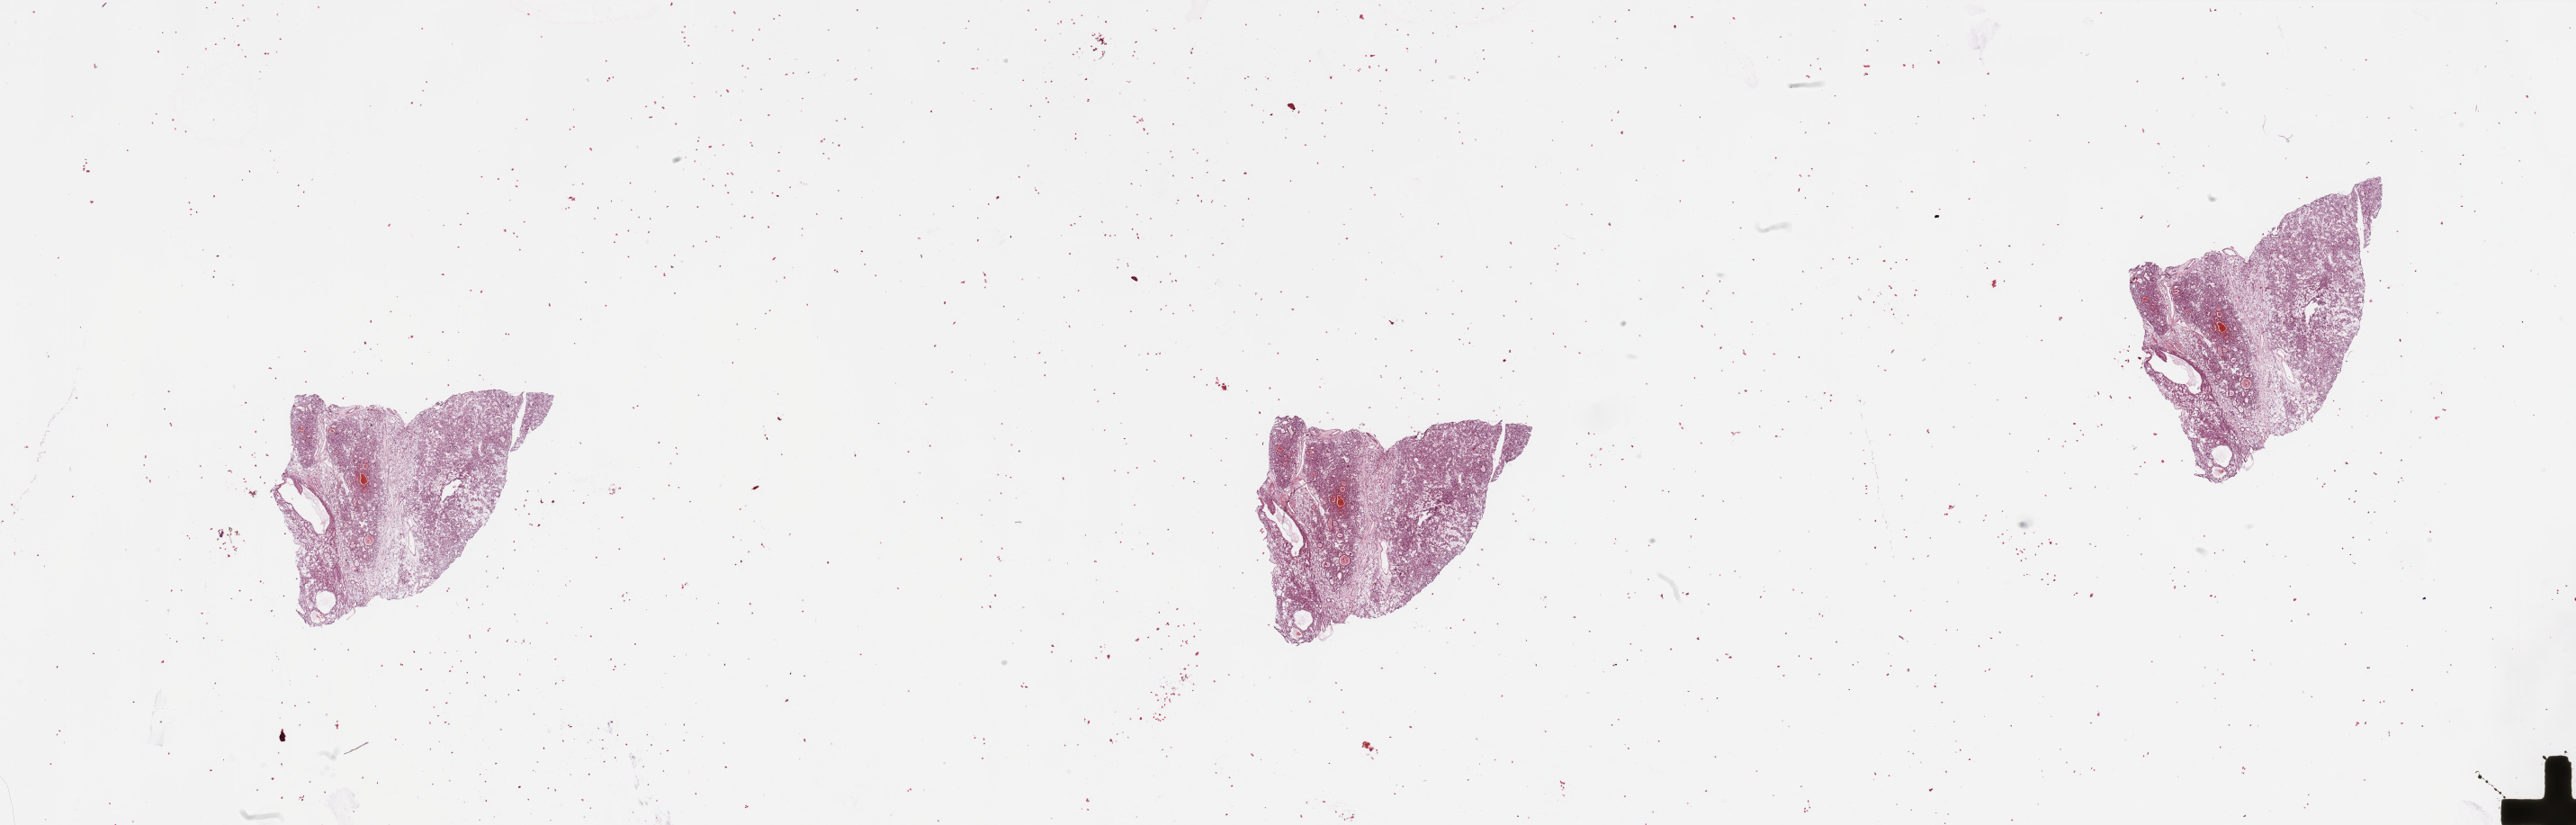
Digitized H&E-stained tissue section (whole slide) — whole scanned area (about 45.3 x 14.5 mm) shown as a low-resolution overview, tumour tissue sample, sampled site: kidney. Patient: male, age 72 years.
Histologic diagnosis: Renal cell carcinoma, NOS.